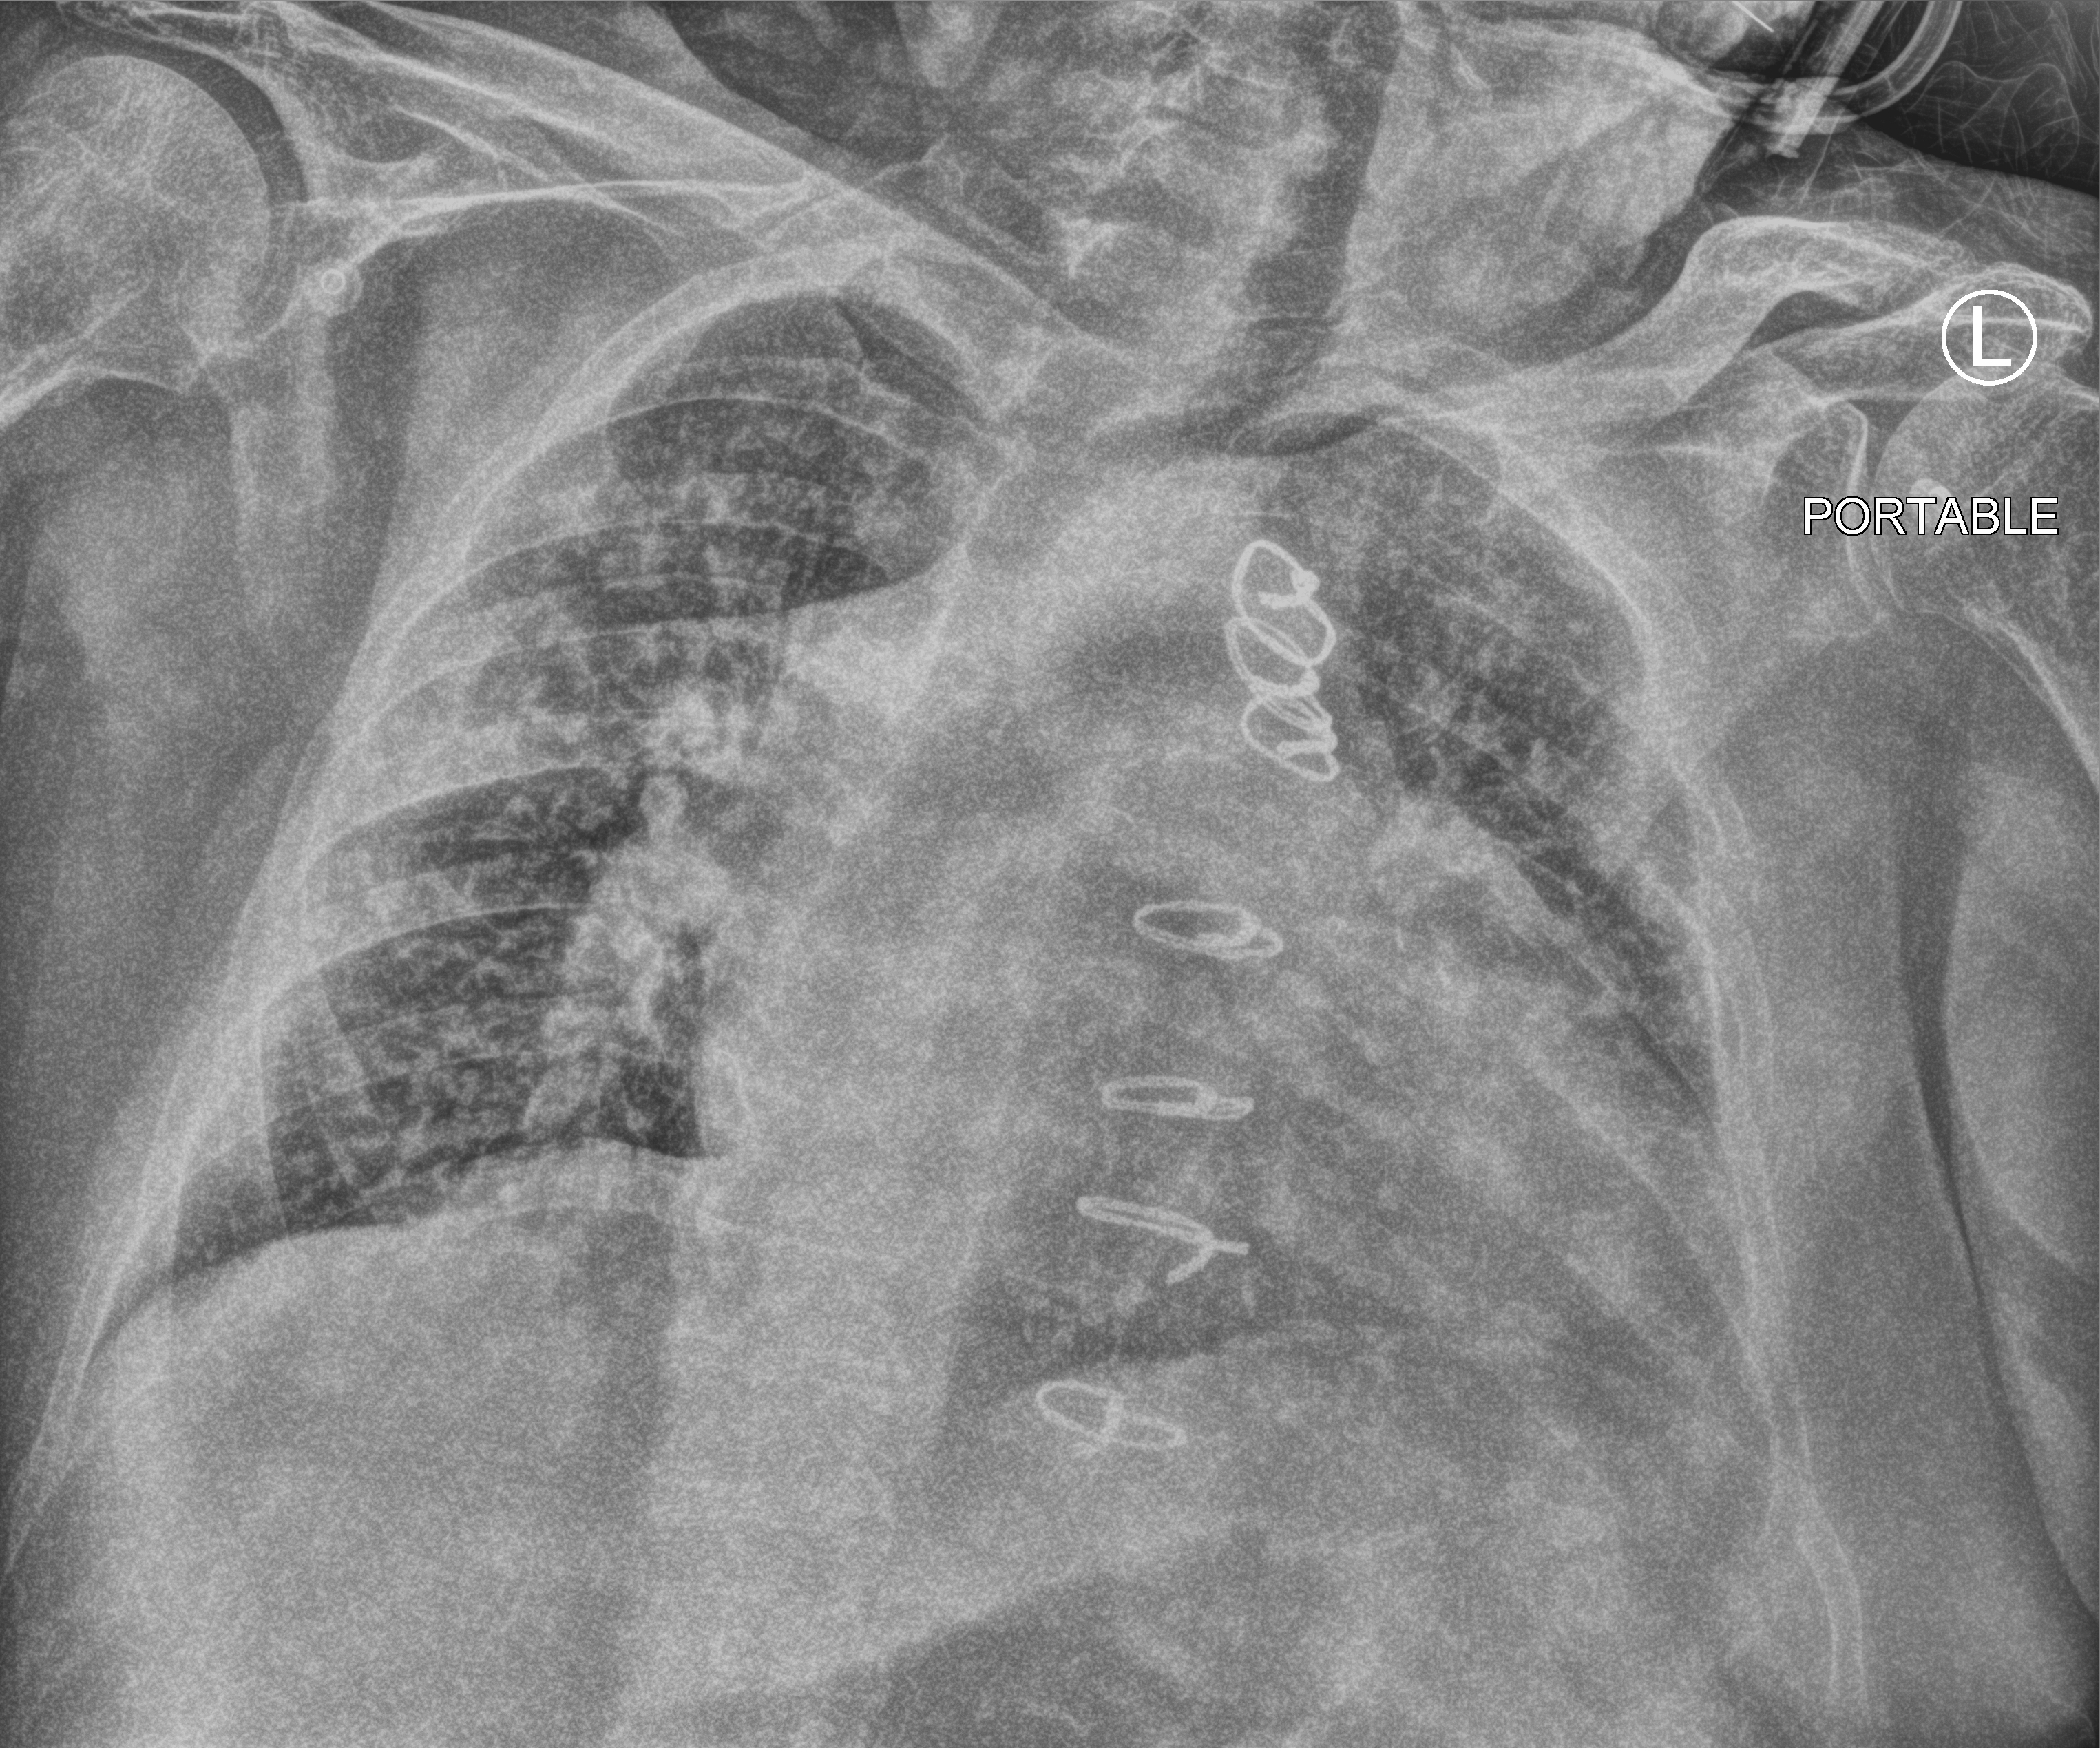
Chest X-ray (portable), anteroposterior (AP) projection. Male patient hospitalised with COVID-19, age 75–90 years.
Hospital-stay facts (about this admission, not read from this image; timing relative to this image not recorded): length of hospital stay: 12 days; chronic kidney disease (admission record): no; admitted to intensive care during this hospital stay: no.